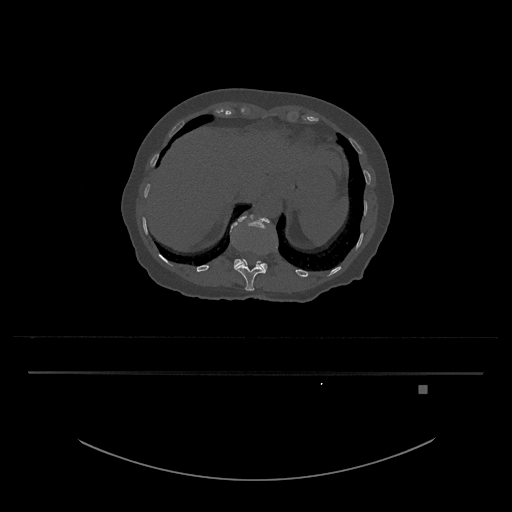
CT including the spine, one axial slice; position 590 of 797 along the scan axis; 120 kVp; bone window (W 1800 / L 400 HU); 0.5 mm slice thickness; 512 × 512 image matrix, field of view 500 × 500 mm. Female patient, age 57 years. Case-level facts recorded for this patient, not image findings: primary cancer: cervical.
Outlined on this slice (semi-automatically segmented with operator editing):
- L1 vertebra: bounding box (x1, y1, x2, y2) in pixels: (231, 215, 270, 271)
- T12 vertebra: (235, 251, 266, 291)